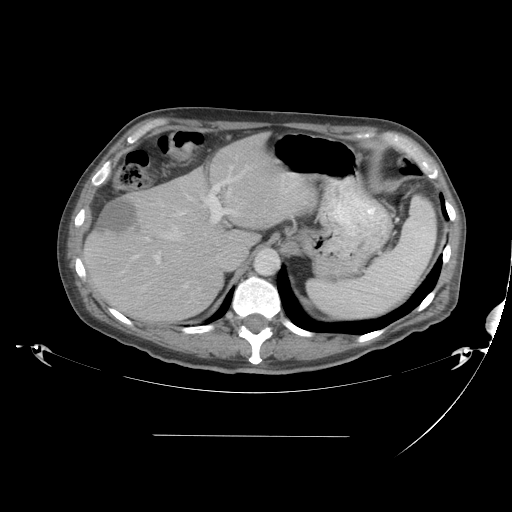
Contrast-enhanced abdominal CT, one axial slice. Position 31 of 48 along the scan axis. Reconstruction kernel STANDARD. Intravenous contrast given. Soft-tissue window (W 400 / L 40 HU). 512 × 512 image matrix, field of view 486 × 486 mm. Male patient, age 65 years. Case-level facts recorded for this patient, not image findings: diagnosis: colorectal cancer liver metastases, imaged before liver resection; multiple liver metastases: yes; largest metastasis: 11 cm; disease in both lobes: yes.
Outlined on this slice (manually delineated by an expert):
- hepatic veins: box from (x=144, y=225) to (x=189, y=289) px
- liver: (x=85, y=134)–(x=312, y=322)
- planned liver remnant (the part of the liver to remain after resection): (x=166, y=134)–(x=312, y=248)
- portal vein (with intrahepatic branches): (x=134, y=165)–(x=250, y=264)
- liver metastasis: (x=94, y=199)–(x=138, y=234)